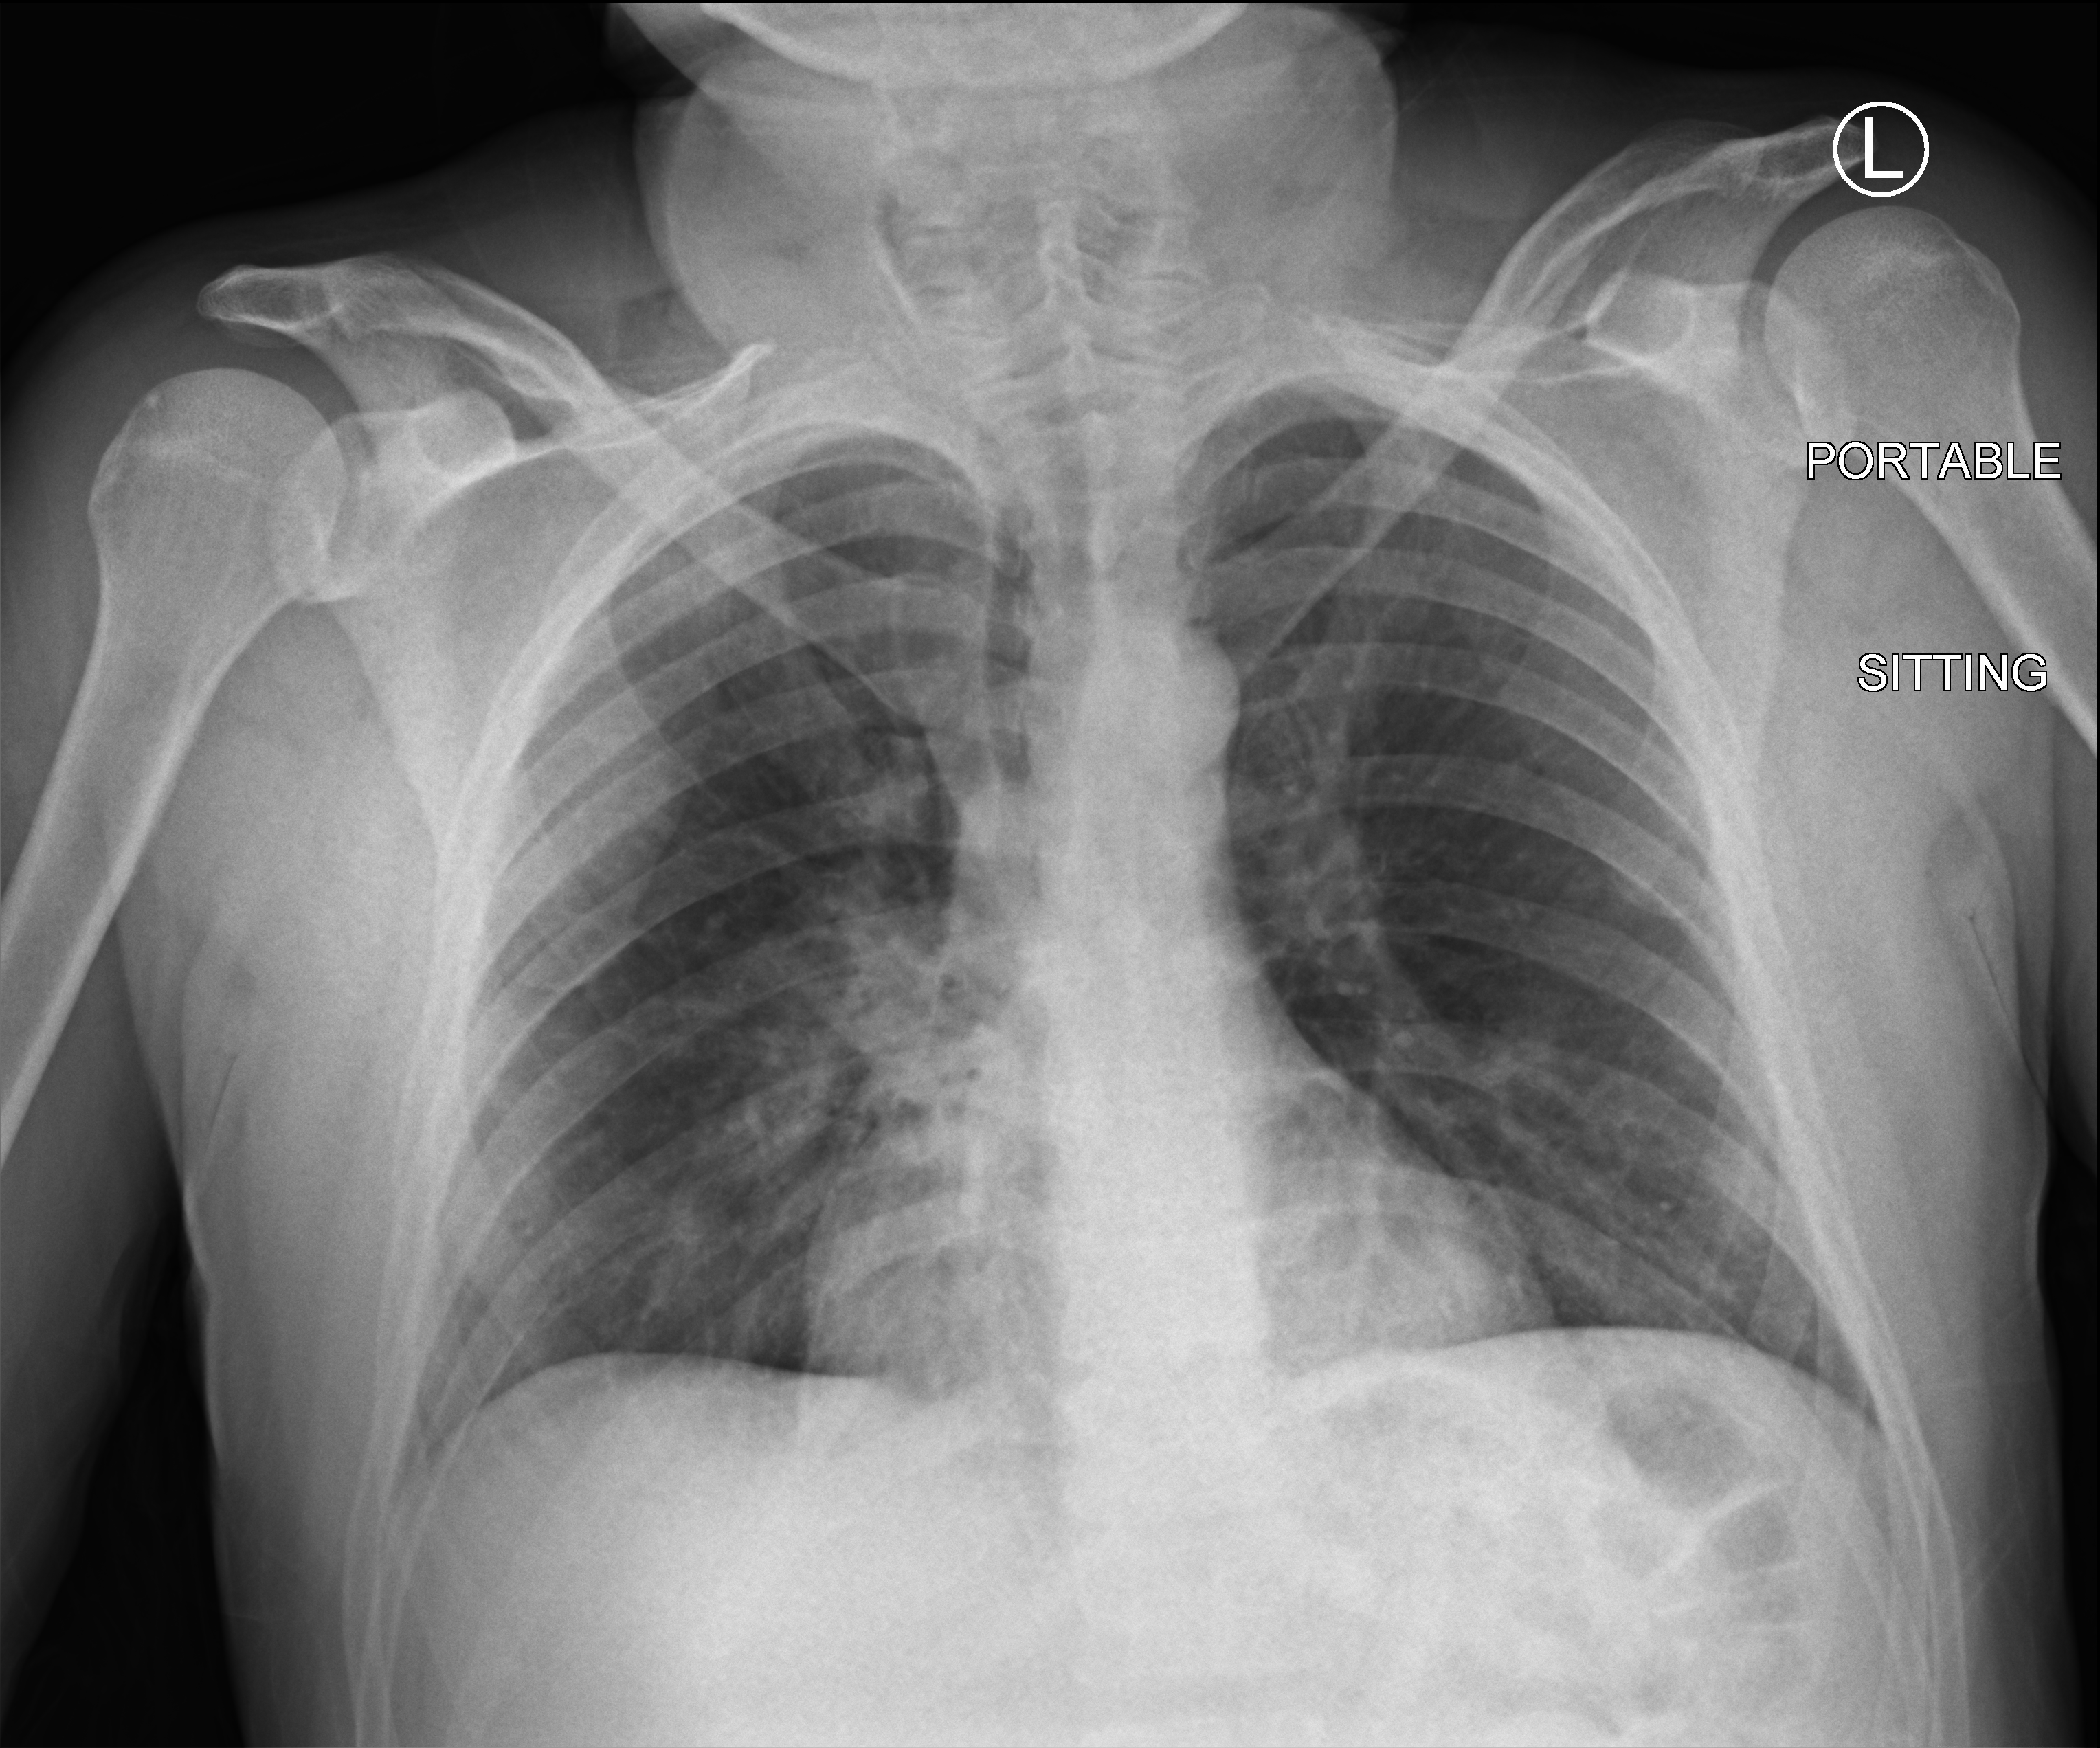
Chest X-ray (portable). Male patient hospitalised with COVID-19, age 18–59 years.
Hospital-stay facts (about this admission, not read from this image; timing relative to this image not recorded): mechanically ventilated during this hospital stay: no.